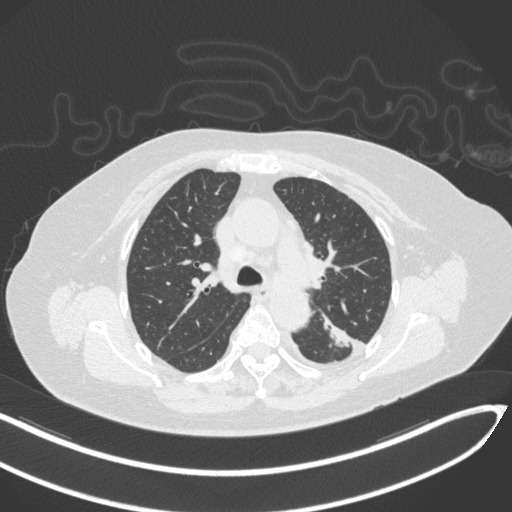
Chest CT, one axial slice. Position 214 of 270 along the scan axis. 120 kVp. Lung window (W 1500 / L -600 HU). 1 mm slice thickness. 512 × 512 image matrix, field of view 400 × 400 mm. Patient: female, 76 years. From the clinical record (not read from this slice): clinical TNM (as recorded): T1c N0 M0.
Outlined on this slice (bounding box drawn by a radiologist):
- lung tumour (recorded histology: adenocarcinoma): bounding box [x1, y1, x2, y2] px = [325, 314, 354, 356]